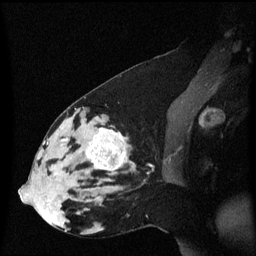
Breast MRI (dynamic contrast-enhanced), one sagittal slice. Dynamic contrast-enhanced series, image 2 of 3 at this slice position (ordered by acquisition). 1.5 T. TE 4.2 ms, TR 8.4 ms. 2 mm slice thickness. 256 × 256 image matrix, field of view 210 × 210 mm. Patient: female, 33 years. From the clinical record (not read from this slice): setting: breast cancer imaged before/during neoadjuvant chemotherapy; receptor status: triple-negative.
Outlined on this slice (semi-automatic segmentation, software-assisted and operator-edited):
- analysis volume of interest (the breast-tissue region the enhancement analysis was run in; not a lesion): bounding box [x1, y1, x2, y2] px = [44, 123, 137, 189]
- tumour enhancement mask (voxels above the 70 % enhancement threshold inside the analysis volume of interest): [63, 129, 127, 171]